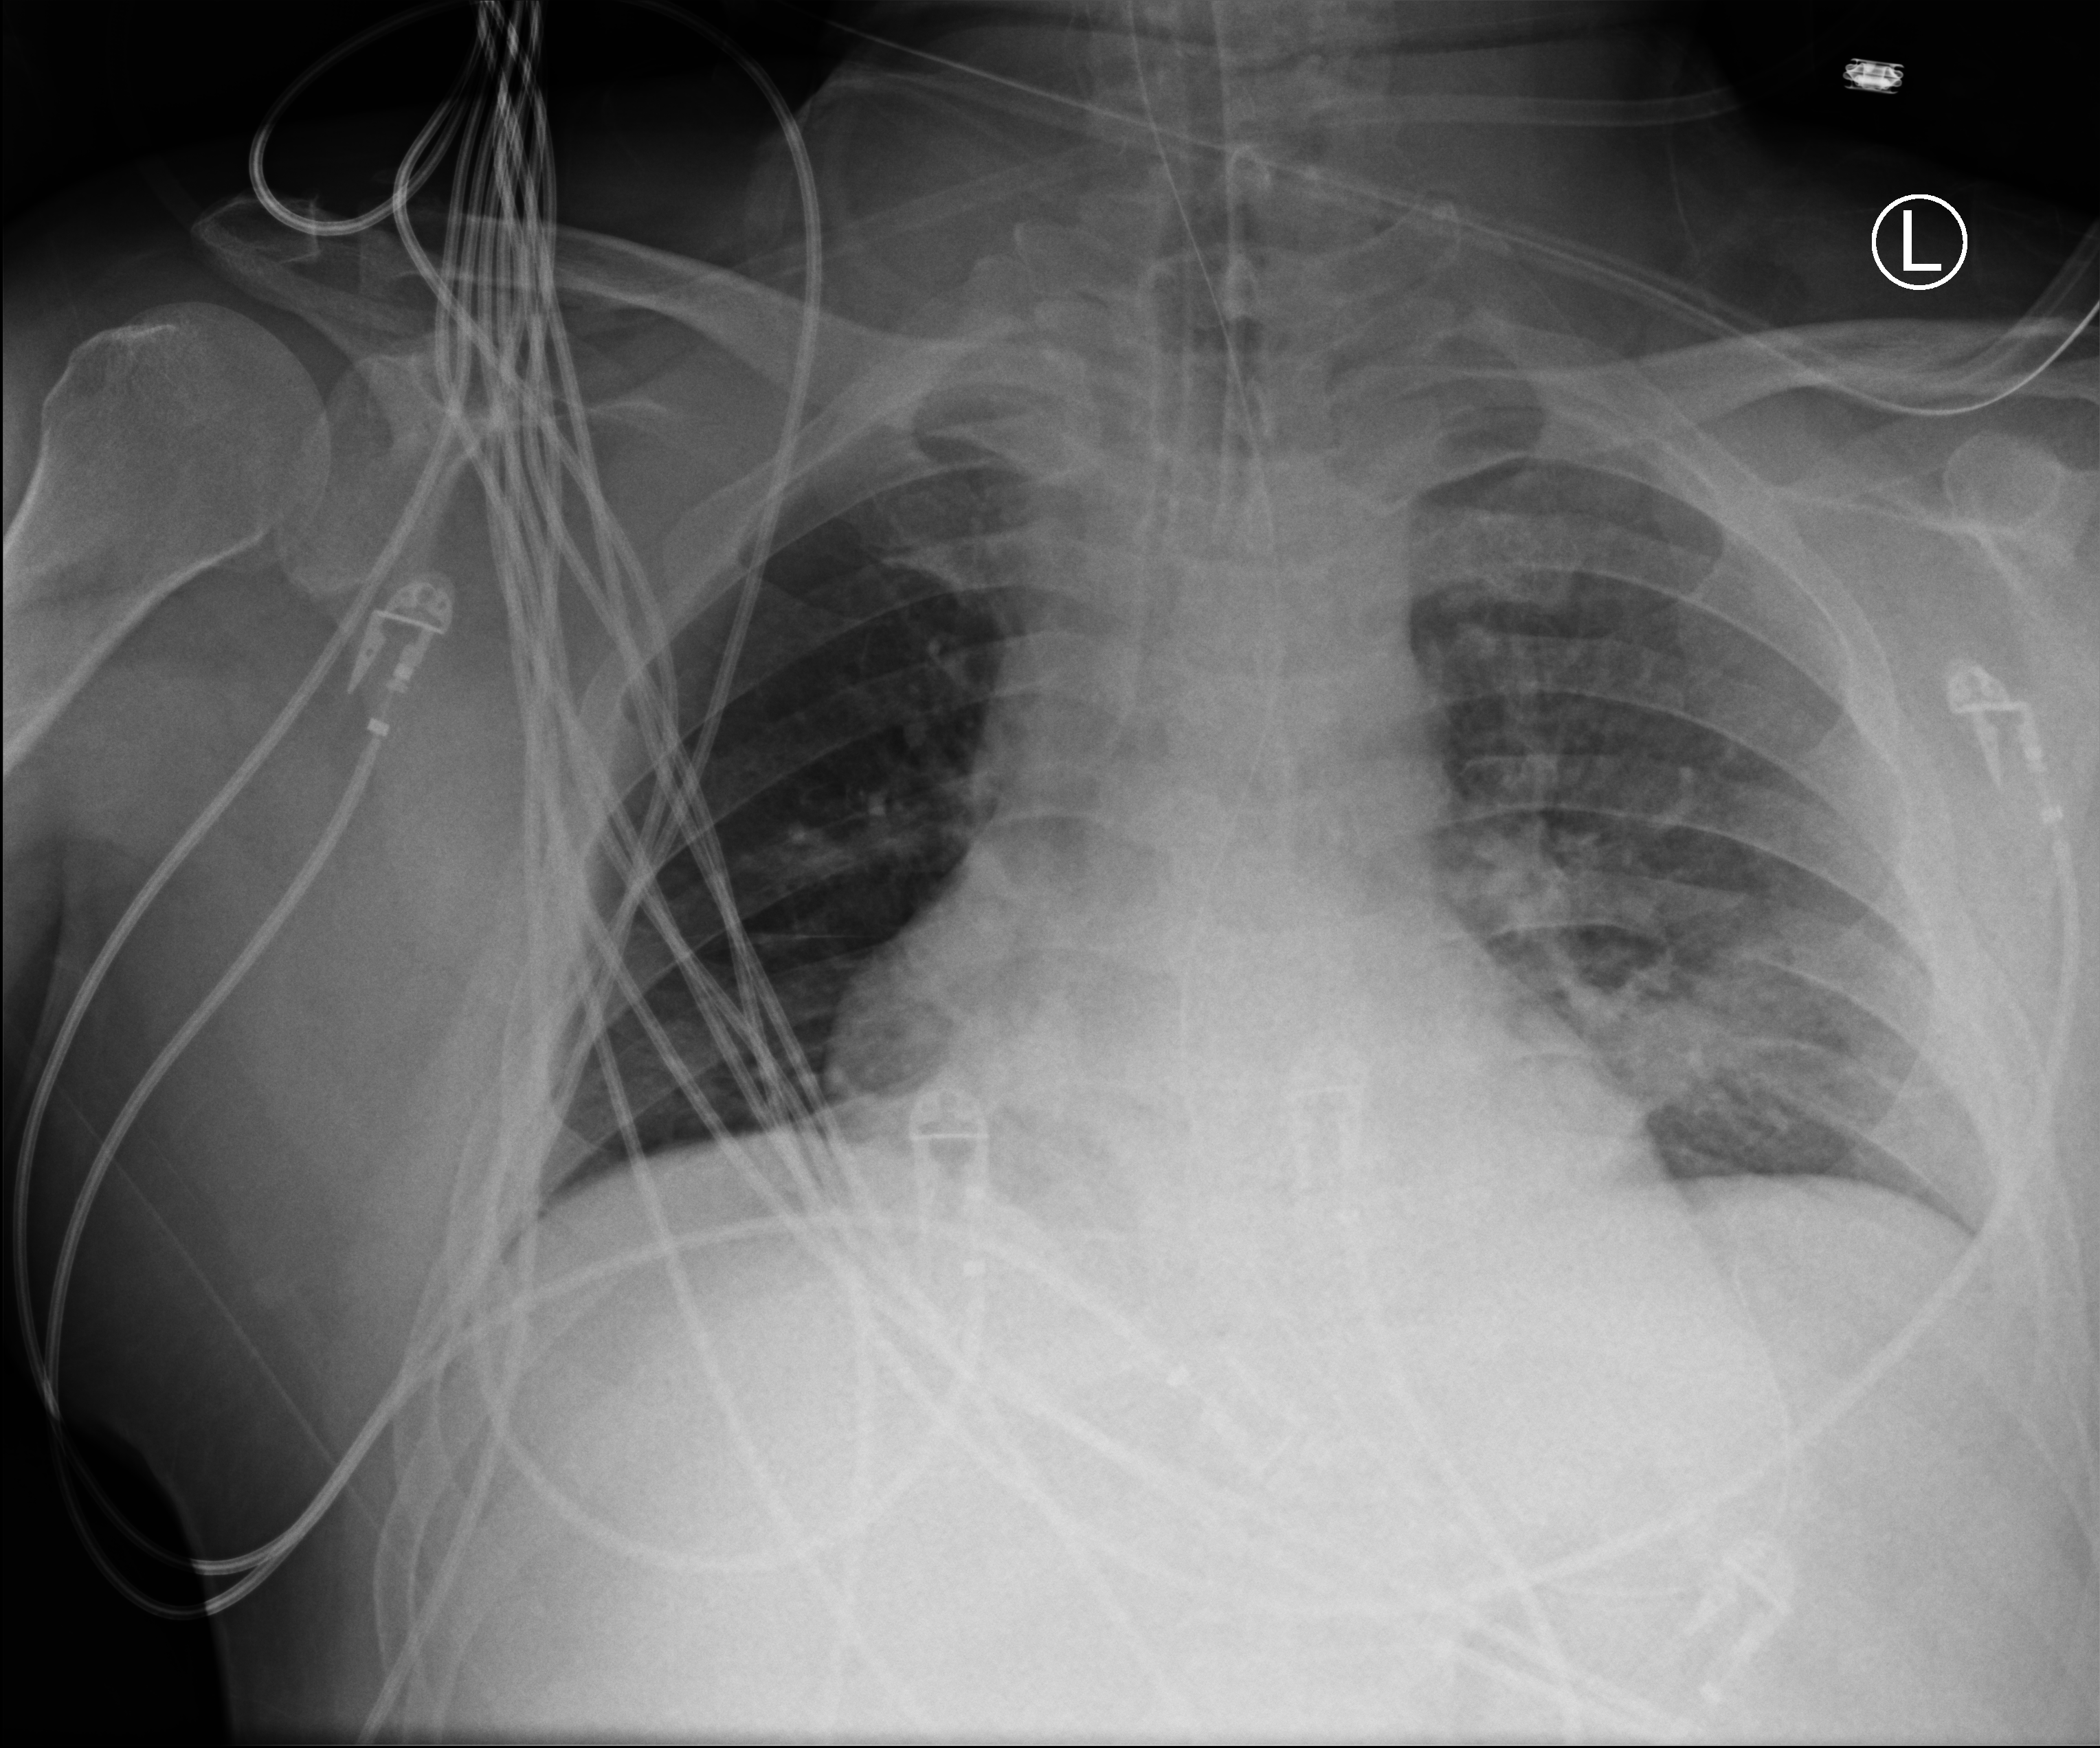
Chest X-ray (portable), anteroposterior (AP) projection. Patient hospitalised with COVID-19; male, aged 18–59 years.
Admission-level facts for this patient (not findings on this image; timing relative to this image not recorded): length of hospital stay: 65 days; admitted to intensive care during this hospital stay: yes.